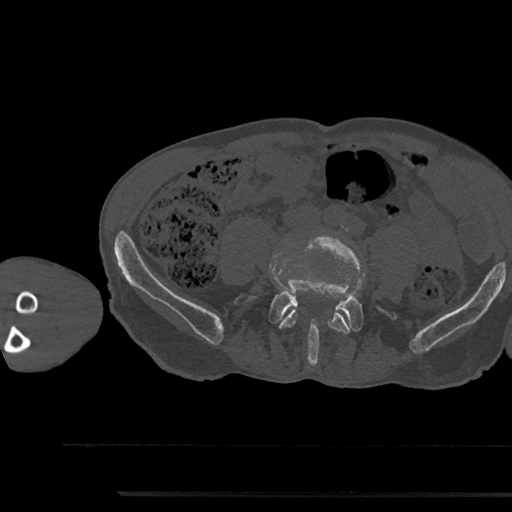
CT including the spine, one axial slice; position 374 of 797 along the scan axis; reconstruction kernel Br40s/3; bone window (W 1800 / L 400 HU); 0.5 mm slice thickness; 512 × 512 image matrix, field of view 367 × 367 mm. Patient: male, 79 years. Case-level facts recorded for this patient, not image findings: primary cancer: prostate.
Annotated regions visible in this slice (semi-automatically segmented with operator editing):
- L4 vertebra: bounding box (x1, y1, x2, y2) in pixels: (279, 235, 364, 334)
- L5 vertebra: (235, 271, 397, 364)